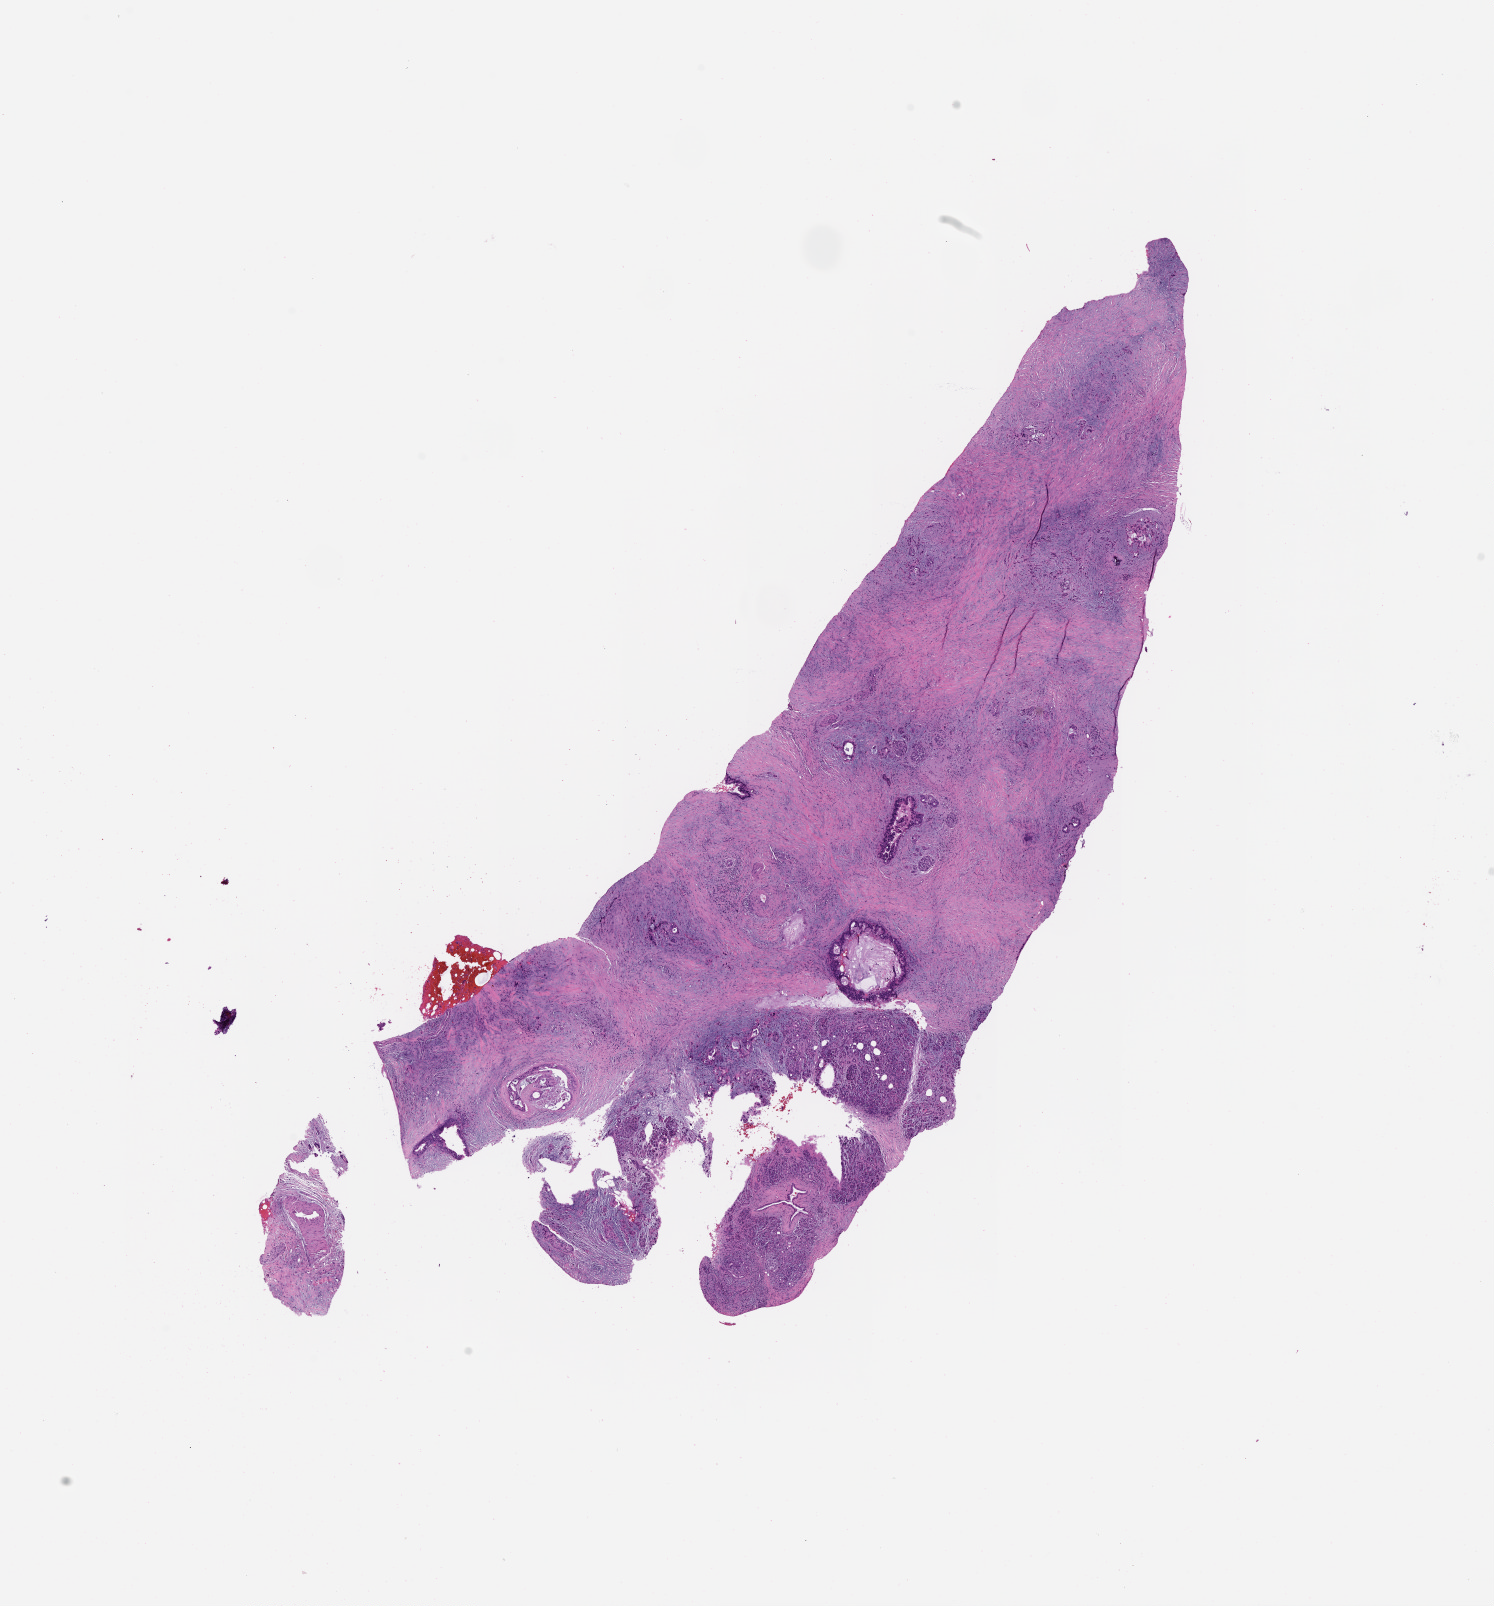
Digitized H&E tissue section (whole slide) — shown as a low-resolution overview of the whole scanned area (about 12.0 x 12.9 mm), tumour tissue sample, pancreas. Patient: female, age 71 years. Histologic grade: G3 (poorly differentiated).
AJCC pathologic stage: IIB. Diagnosis: Infiltrating duct carcinoma, NOS. Primary tumour site (as recorded): head.